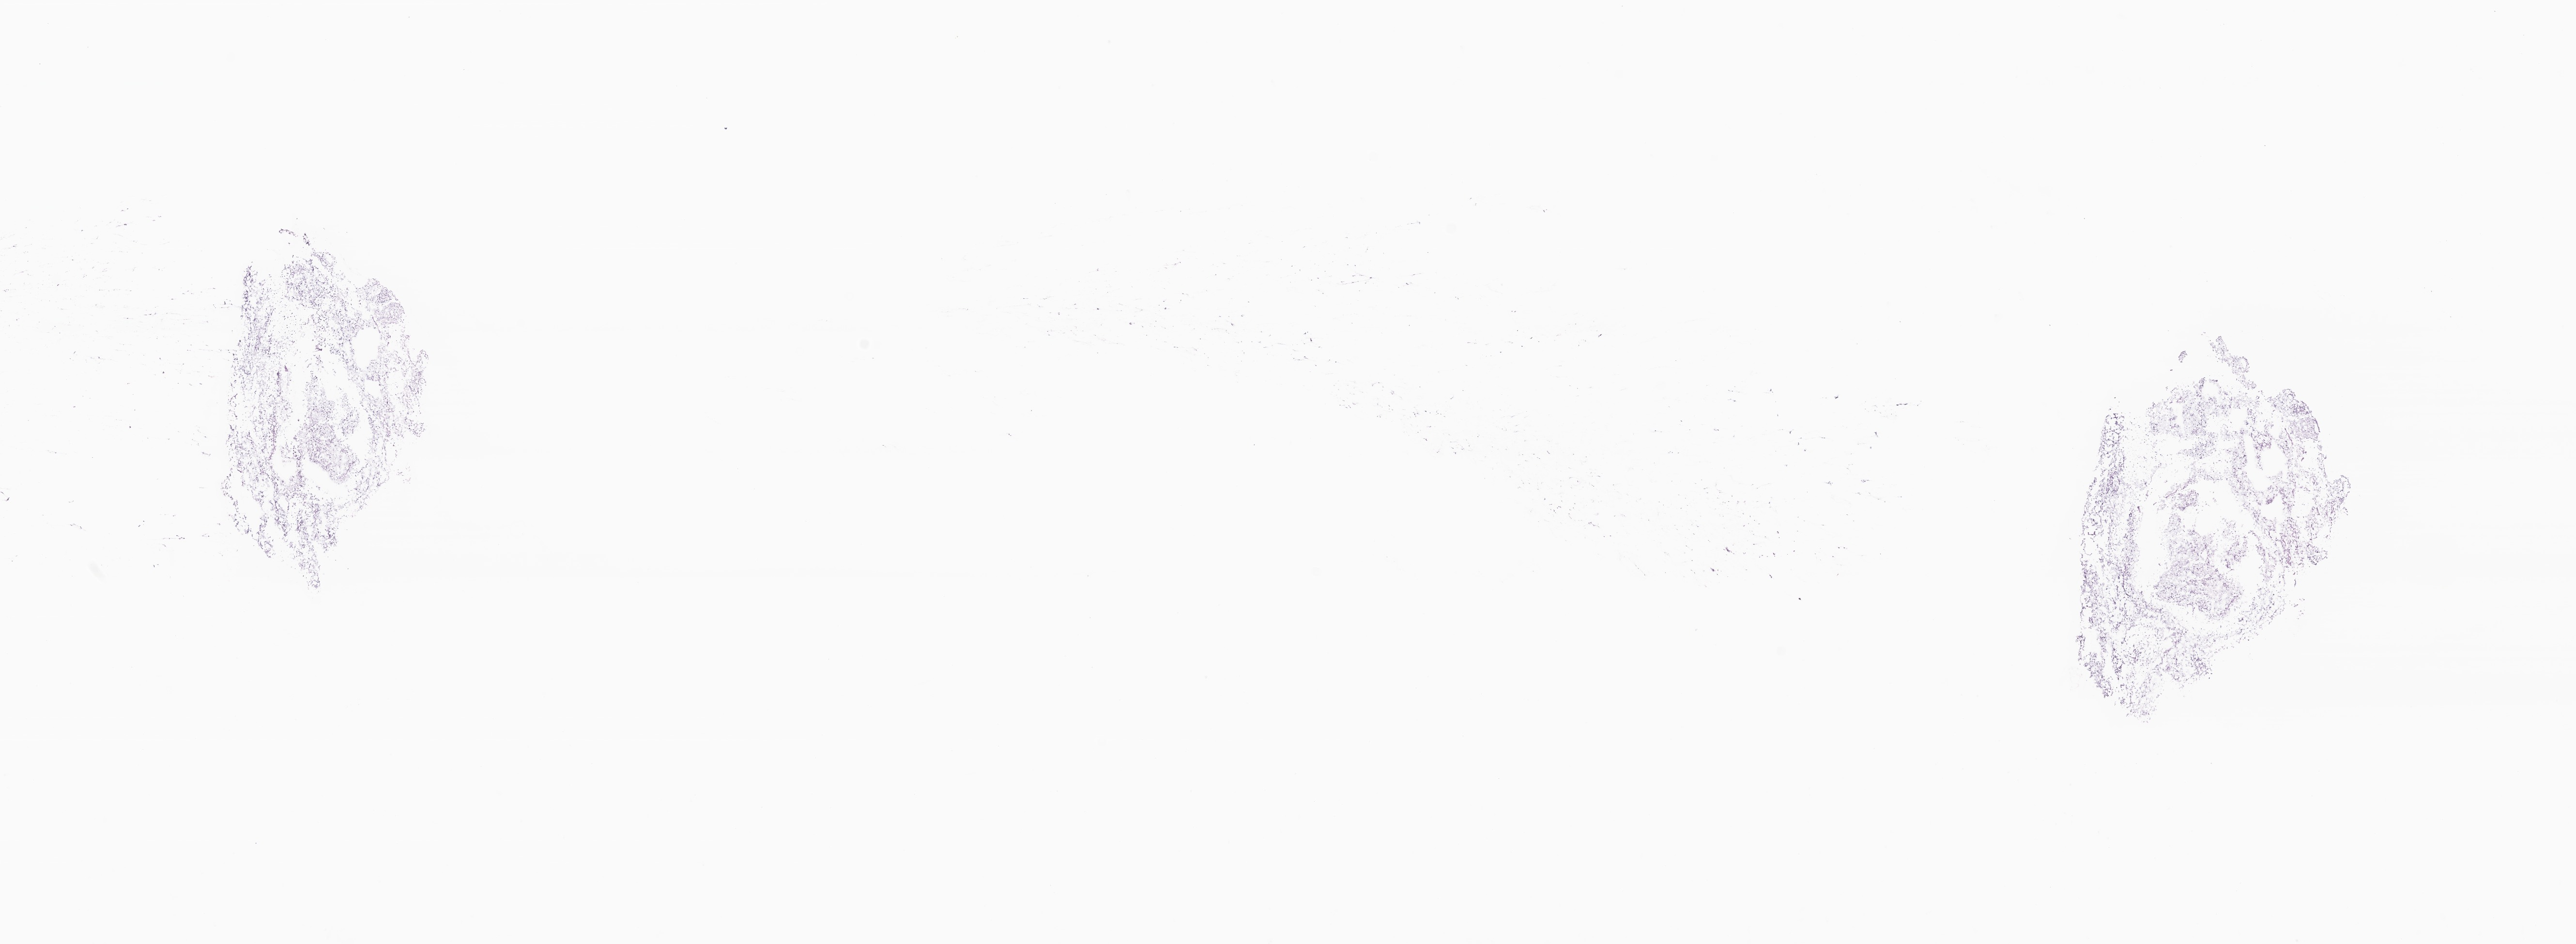
Whole-slide image, haematoxylin and eosin stain of tumor tissue from the brain, low-resolution overview of the scanned area, about 22.4 x 8.2 mm; cryosection (OCT / tissue freezing medium). Patient: male, age 251 days.
Diagnosis: Astrocytoma, NOS.